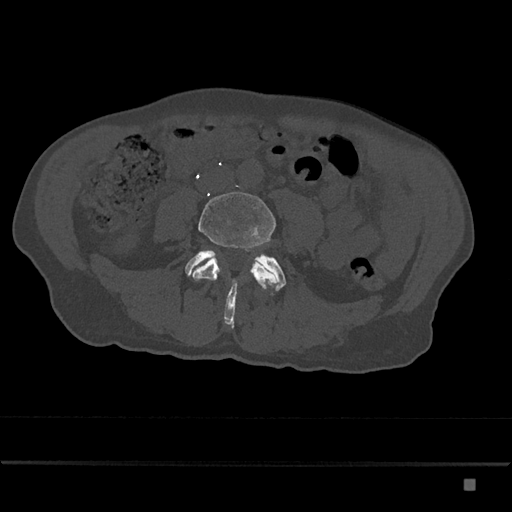
CT including the spine, one axial slice. Slice 316 of 797 in the series (ordered by position). Reconstruction kernel Br40s/3. 120 kVp. Bone window (W 1800 / L 400 HU). 0.5 mm slice thickness. 512 × 512 image matrix, field of view 390 × 390 mm. Patient: male, 72 years. From the clinical record (not read from this slice): primary cancer: prostate.
Outlined on this slice (semi-automatically segmented with operator editing):
- L4 vertebra: bounding box (x1, y1, x2, y2) in pixels: (190, 192, 277, 289)
- L5 vertebra: (185, 250, 286, 328)